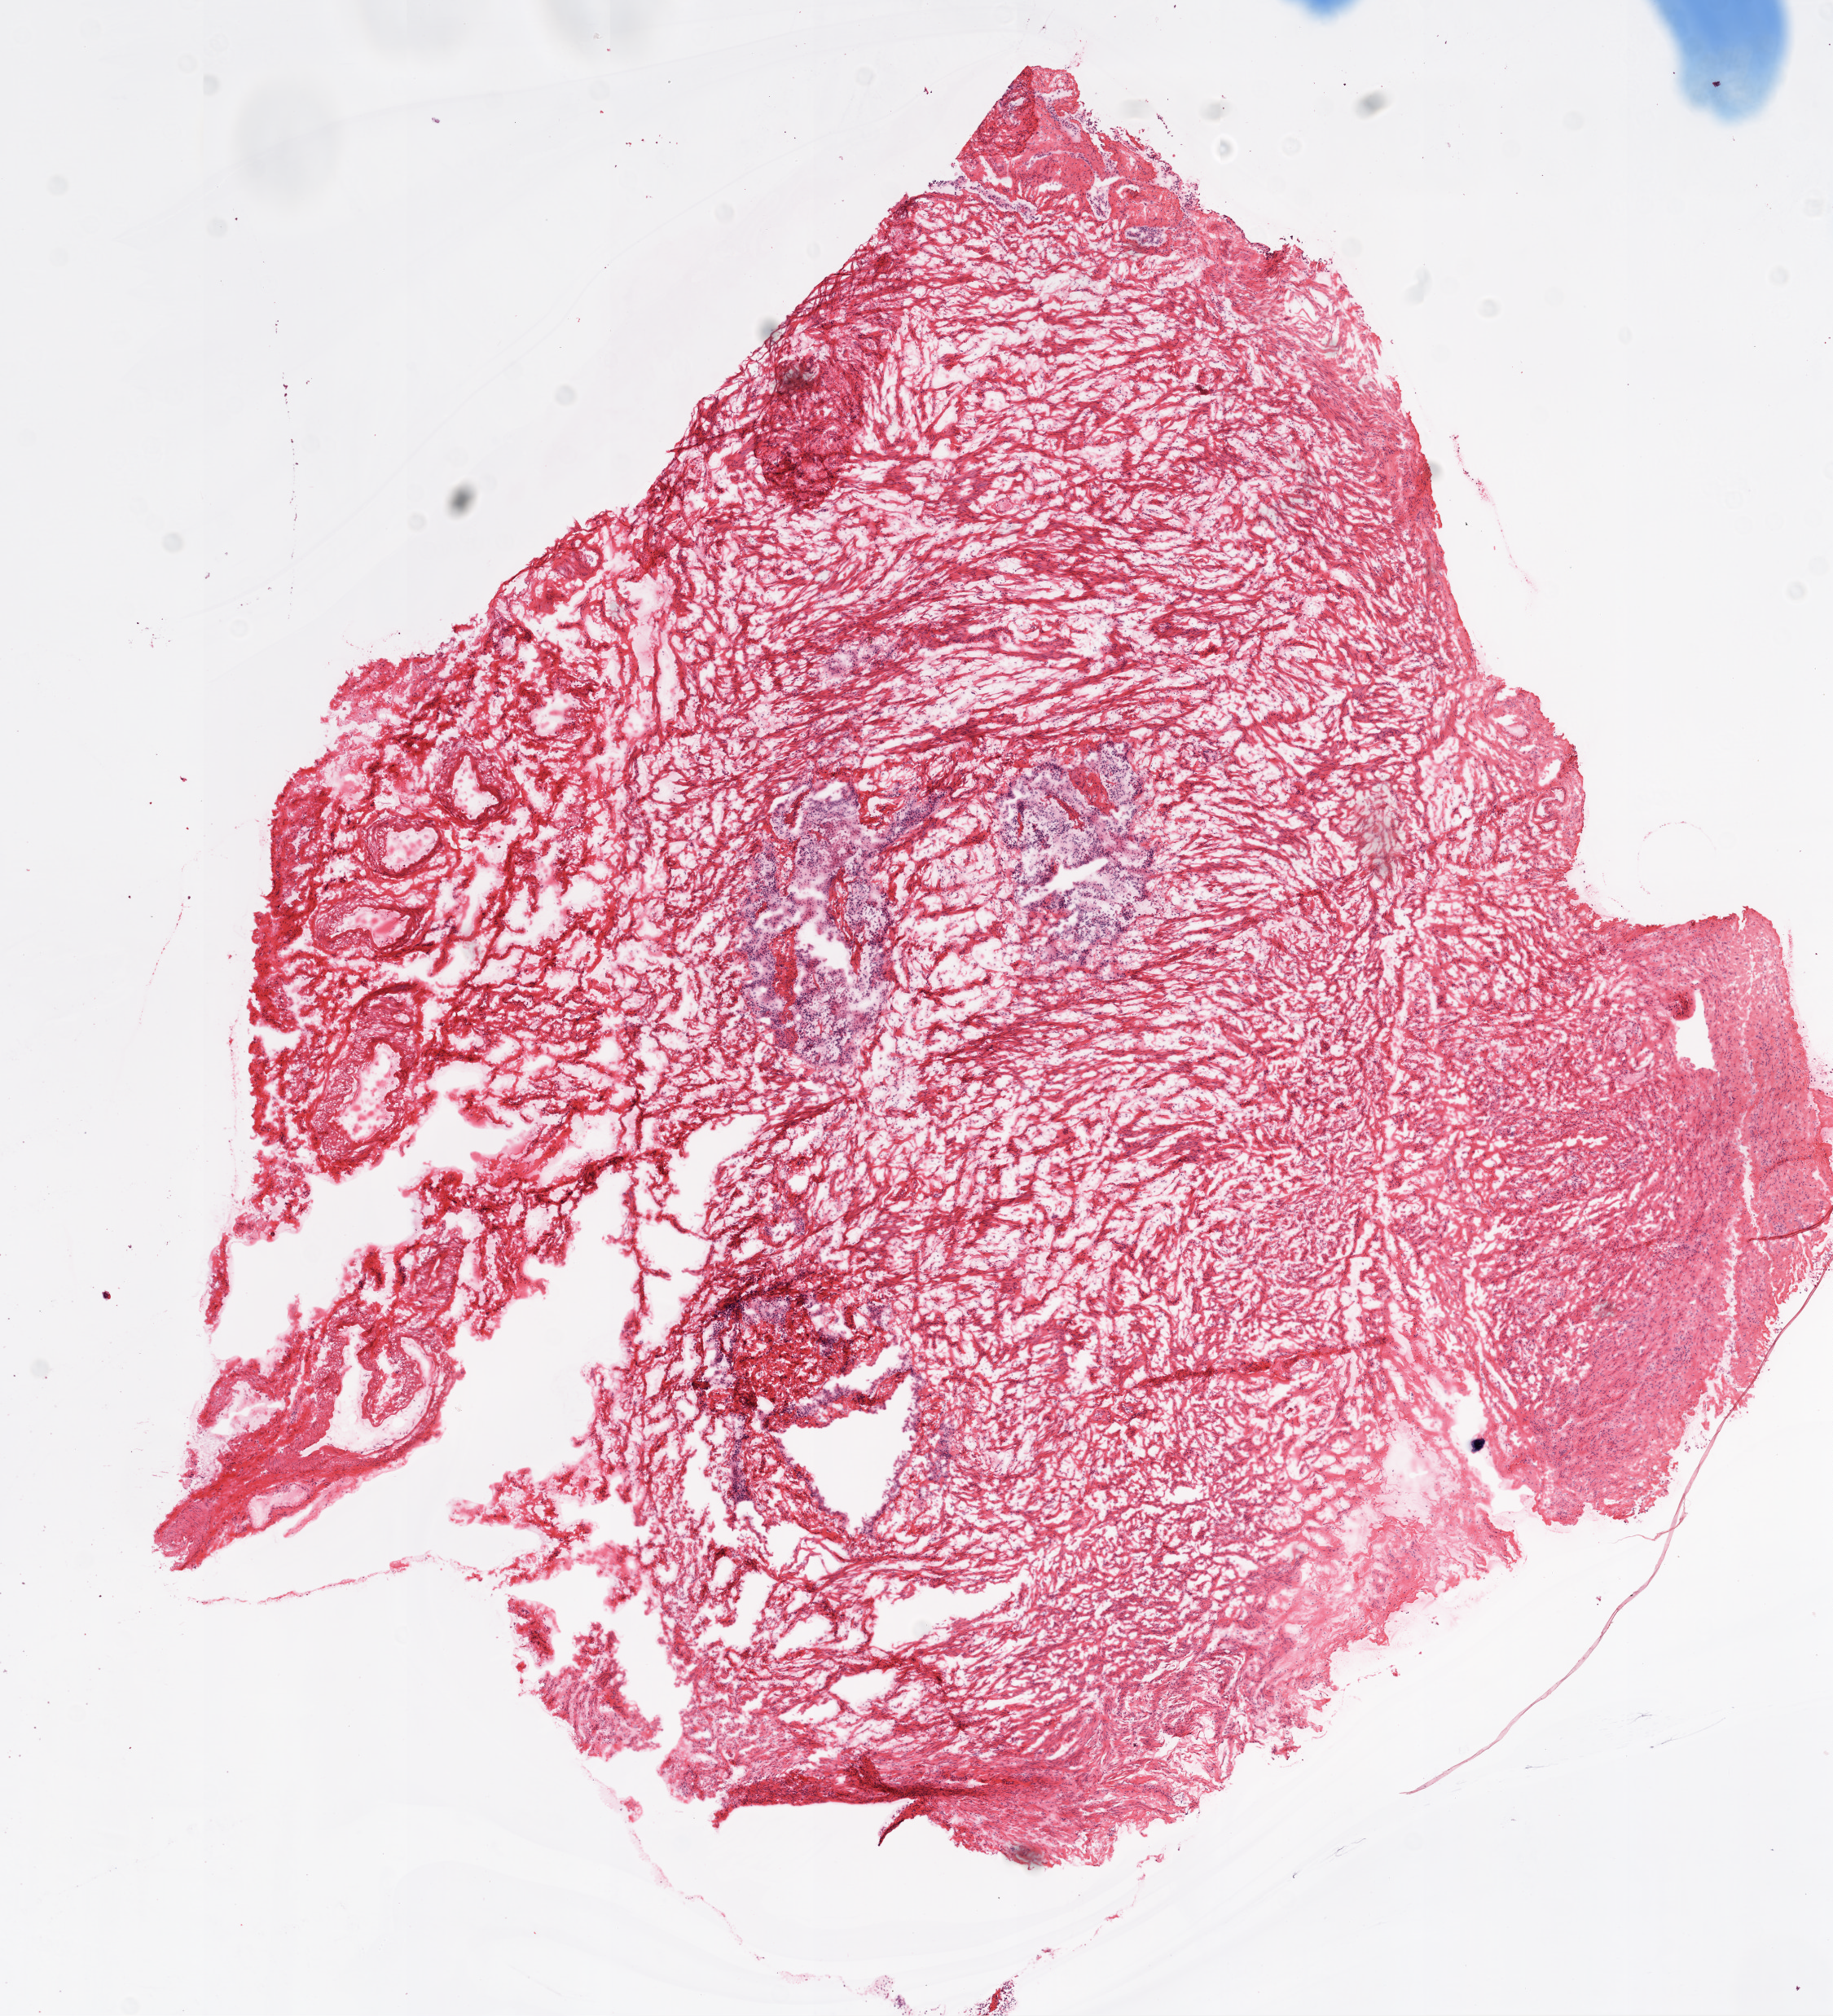
Whole-slide histology image, H&E-stained, a low-resolution overview of the entire scanned area, about 9.0 x 9.9 mm, frozen section, ovary, solid tissue normal (non-tumour tissue) sample. Patient: female, age at initial diagnosis 55 years.
This section: solid tissue normal (non-tumour) sample from the same patient. Patient diagnosis: Serous cystadenocarcinoma, NOS.